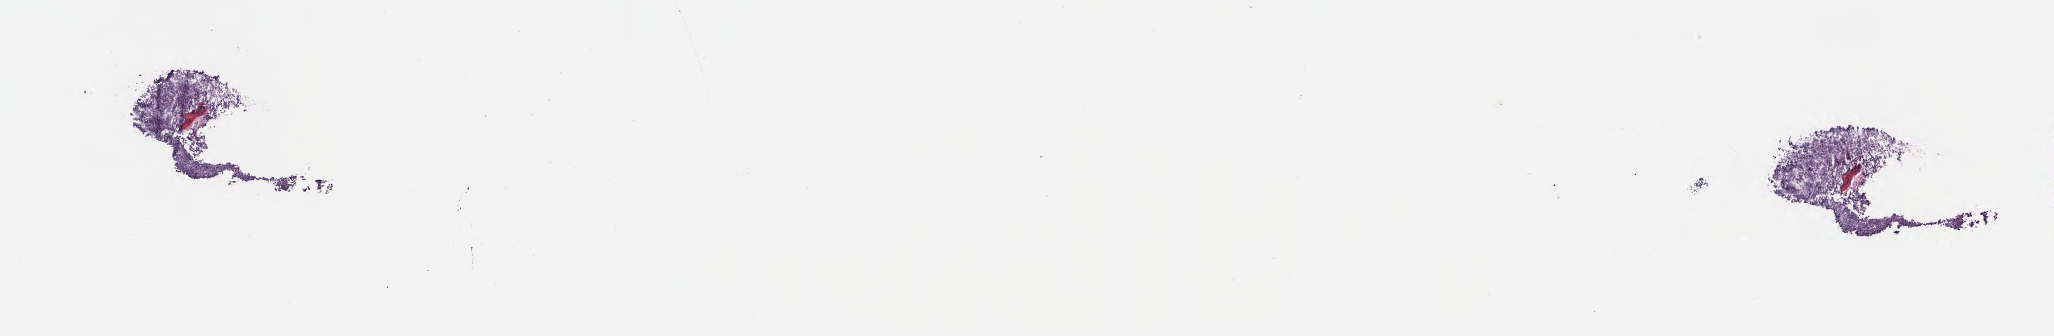
Hematoxylin and eosin (H&E) whole-slide image, whole scanned area (about 16.6 x 2.7 mm) shown as a low-resolution overview. Frozen section (tissue freezing medium). Primary tumor. Patient: male, aged 15. Slide review estimates, as recorded: tumor cells 85%, tumor nuclei 90%, stromal cells 5%, necrosis 10%, normal cells 0%. Infiltration values recorded for this section: lymphocyte infiltration 50%, monocyte infiltration 25%, neutrophil infiltration 5%.
- diagnosis: Burkitt lymphoma, NOS
- section: top of the tissue portion
- Ann Arbor stage (patient): Stage IV